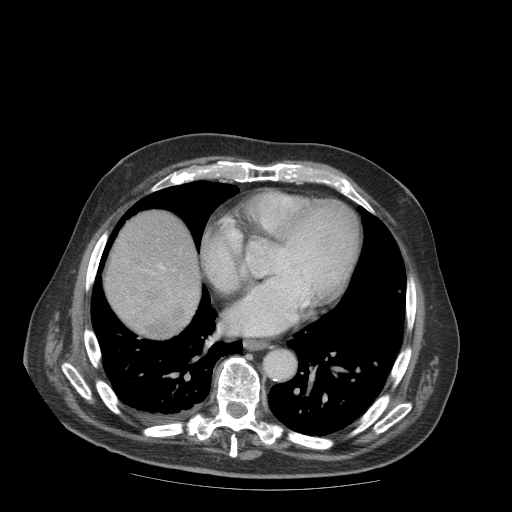
Contrast-enhanced abdominal CT (liver protocol), one axial slice; position 90 of 99 along the scan axis; reconstruction kernel STANDARD; soft-tissue window (W 400 / L 40 HU); 2.5 mm slice thickness; 512 × 512 image matrix, field of view 420 × 420 mm. From the clinical record (not read from this slice): diagnosis: hepatocellular carcinoma (patient treated with transarterial chemoembolisation; whether this scan precedes or follows treatment is not stated here); TNM stage (as recorded): Stage-IIIB; Child-Pugh class: A; tumour differentiation: well differentiated; tumour nodularity: multinodular.
Structures marked on this image (semi-automatically segmented with operator editing):
- abdominal aorta: bounding box [x1, y1, x2, y2] px = [264, 350, 295, 378]
- liver parenchyma outside the tumour (the mass and vessels are separate outlines, so this box may not span the whole liver): [104, 210, 200, 322]
- mass: [106, 257, 197, 339]
- liver vessels: [159, 265, 162, 268]